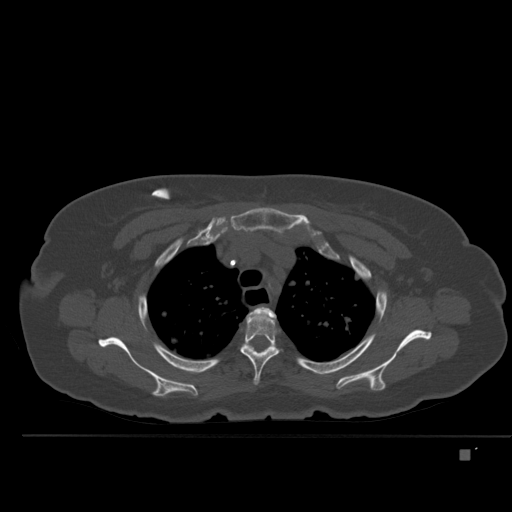
CT including the spine, one axial slice. Position 379 of 477 along the scan axis. Bone window (W 1800 / L 400 HU). 1.5 mm slice thickness. 512 × 512 image matrix, field of view 422 × 422 mm. Female patient, age 74 years. From the clinical record (not read from this slice): primary cancer: colon.
Outlined on this slice (semi-automatically segmented with operator editing):
- T2 vertebra: bounding box [x1, y1, x2, y2] px = [253, 306, 276, 317]
- T3 vertebra: [240, 307, 279, 385]